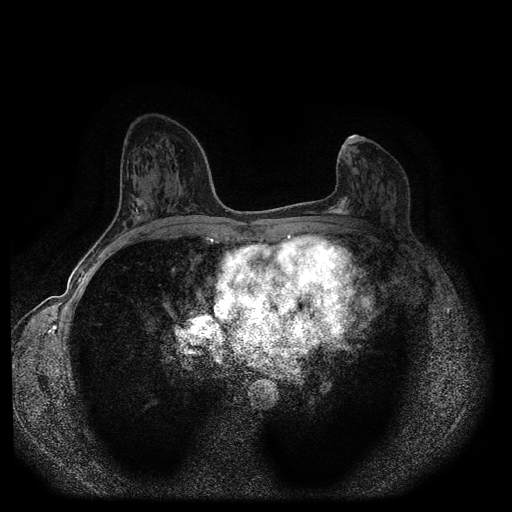
Breast MRI (dynamic contrast-enhanced, multi-phase), one axial slice; dynamic contrast-enhanced series, time point 2 of 5 at this slice position (early post-contrast); 1.5 T; TE 2.6 ms, TR 5.4 ms; 2 mm slice thickness; 512 × 512 image matrix, field of view 340 × 340 mm. Female patient, age 57 years.
Annotated regions visible in this slice (semi-automatic segmentation, software-assisted and operator-edited):
- breast lesion (labelled 'tumour' in the annotation; benign lesions carry a separate 'benign' label): bounding box <325,196,352,217> (left, top, right, bottom; pixels)